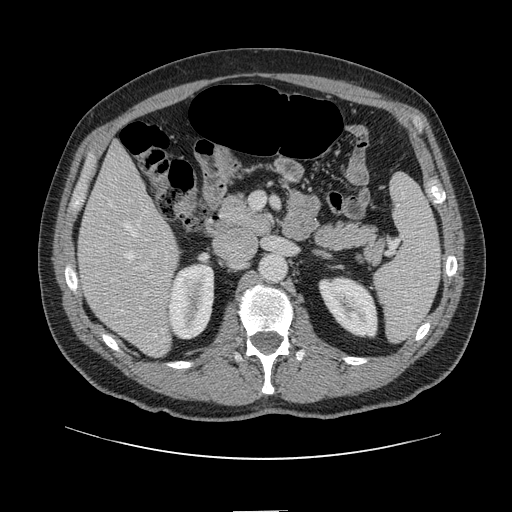
Contrast-enhanced abdominal CT, one axial slice; slice 55 of 161 in the series (ordered by position); 120 kVp; intravenous contrast given; soft-tissue window (W 400 / L 40 HU); 2.5 mm slice thickness; 512 × 512 image matrix, field of view 412 × 412 mm. Male patient, age 66 years. From the clinical record (not read from this slice): diagnosis: colorectal cancer liver metastases, imaged before liver resection; multiple liver metastases: no; largest metastasis: 3.5 cm; disease in both lobes: no.
Annotated regions visible in this slice (outlined manually by an expert reader):
- hepatic veins: box from (x=111, y=204) to (x=157, y=336) px
- liver: (x=79, y=144)–(x=179, y=357)
- planned liver remnant (the part of the liver to remain after resection): (x=79, y=145)–(x=166, y=279)
- portal vein (with intrahepatic branches): (x=128, y=249)–(x=158, y=297)